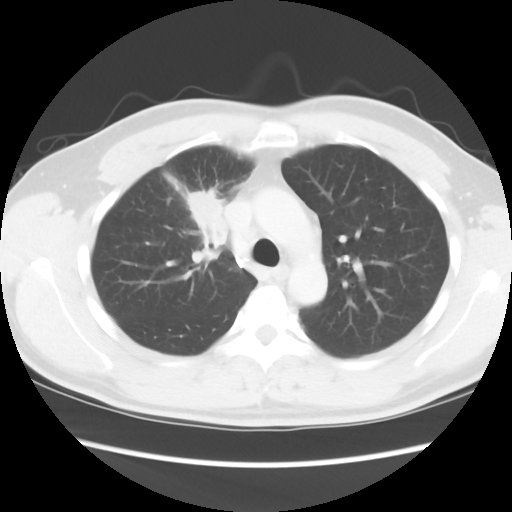
Chest CT, one axial slice. Position 63 of 80 along the scan axis. 120 kVp. Lung window (W 1500 / L -600 HU). 512 × 512 image matrix. Male patient, age 35 years. Case-level facts recorded for this patient, not image findings: clinical TNM (as recorded): T1c N1 M1b.
Structures marked on this image (bounding box drawn by a radiologist):
- lung tumour (recorded histology: adenocarcinoma): bounding box <181,183,230,251> (left, top, right, bottom; pixels)